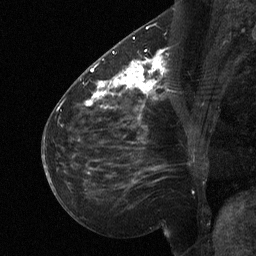
Breast MRI (dynamic contrast-enhanced), one sagittal slice; position 28 of 64 along the scan axis; dynamic contrast-enhanced study with each time point stored as its own series, time point 2 of 3 at this slice position (early post-contrast, ordered by acquisition time); 1.5 T; TE 4.8 ms, TR 27 ms; 2 mm slice thickness; 256 × 256 image matrix, field of view 200 × 200 mm. Female patient, age 51 years. Case-level facts recorded for this patient, not image findings: setting: breast cancer imaged before/during neoadjuvant chemotherapy; receptor status: HR-positive, HER2-negative.
Outlined on this slice (semi-automatically segmented with operator editing):
- analysis volume of interest (the breast-tissue region the enhancement analysis was run in; not a lesion): bounding box <112,46,169,106> (left, top, right, bottom; pixels)
- tumour enhancement mask (voxels above the 90 % enhancement threshold inside the analysis volume of interest): <112,51,167,95>